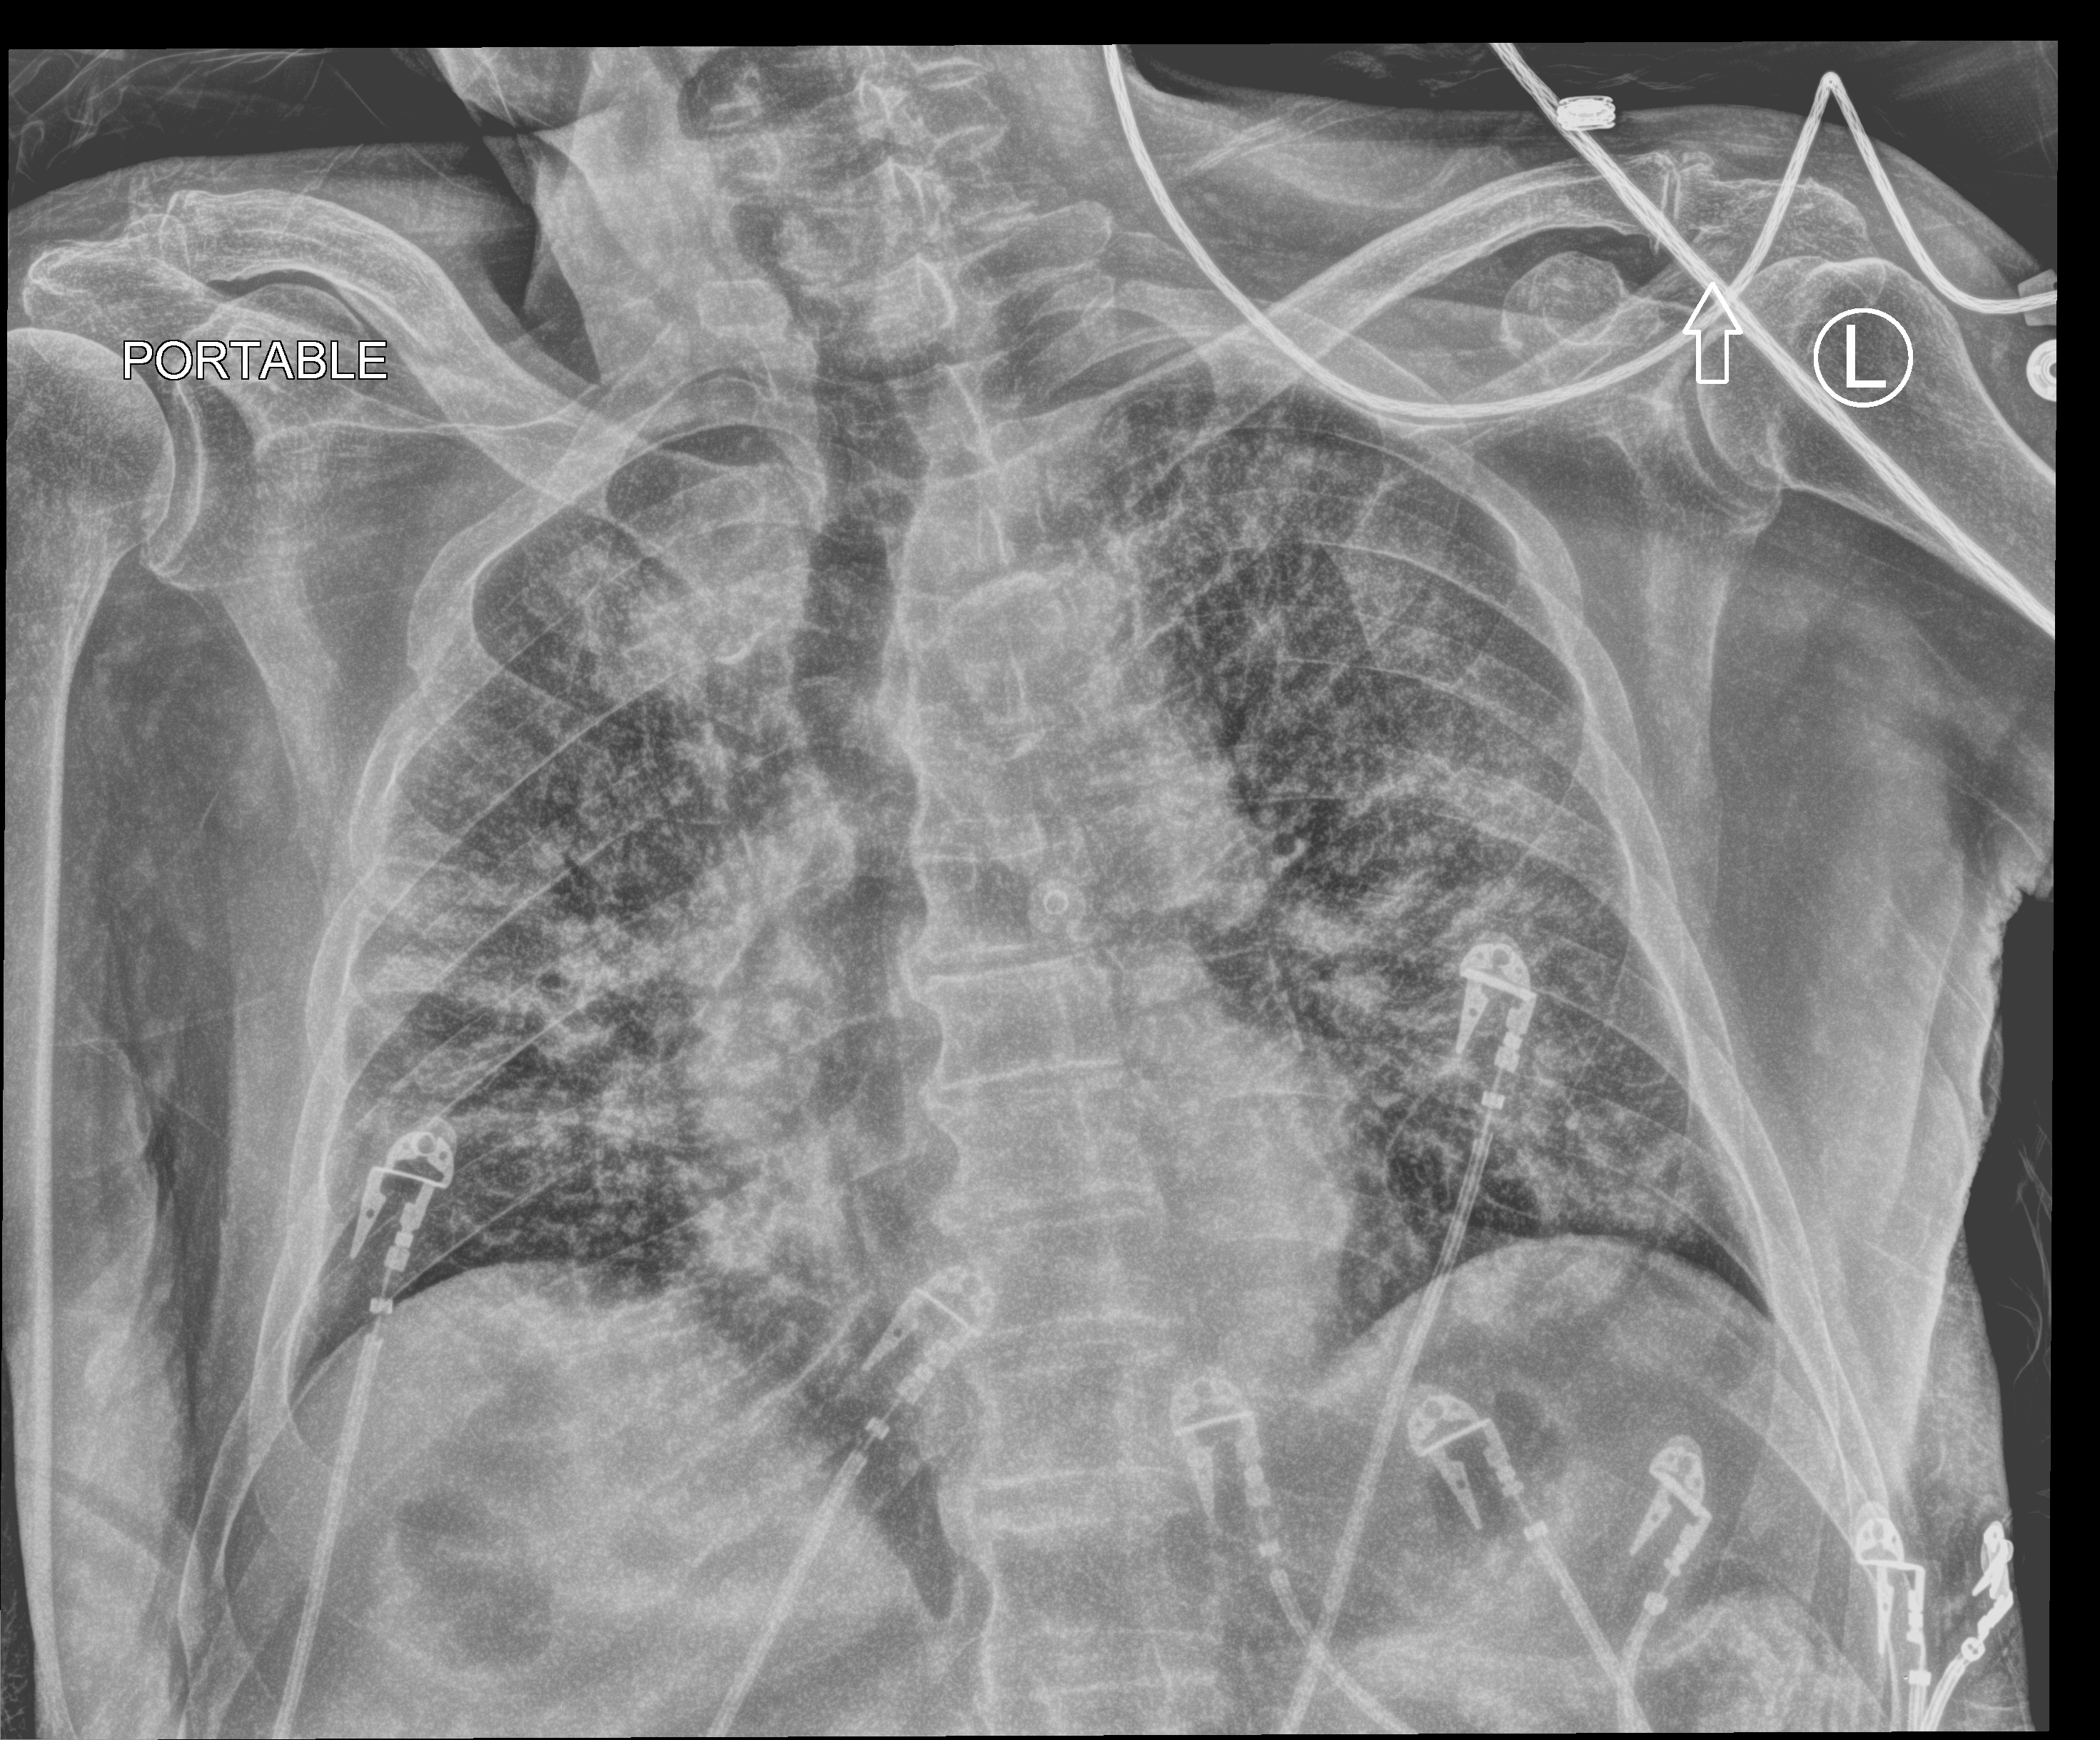
Chest X-ray (portable); anteroposterior (AP) projection. Male patient hospitalised with COVID-19, age 75–90 years.
Admission-level facts for this patient (not findings on this image; timing relative to this image not recorded): mechanically ventilated during this hospital stay: no.